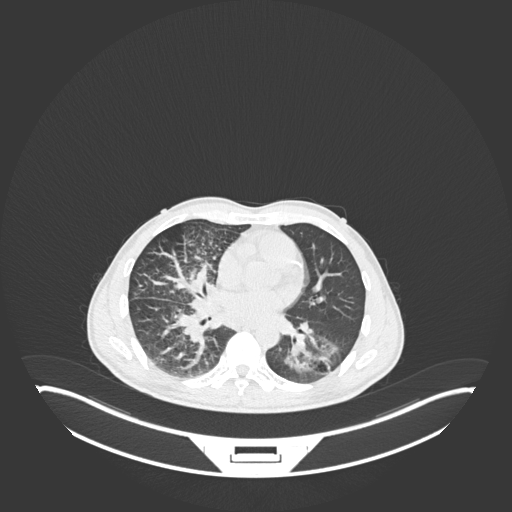
Chest CT, one axial slice; position 112 of 237 along the scan axis; 120 kVp; lung window (W 1500 / L -600 HU); 512 × 512 image matrix, field of view 500 × 500 mm. Patient: male, 49 years. Case-level facts recorded for this patient, not image findings: clinical TNM (as recorded): T2b N1 M0.
Annotated regions visible in this slice (rectangle marked by the reading radiologist):
- lung tumour (recorded histology: adenocarcinoma): bounding box [x1, y1, x2, y2] px = [283, 322, 343, 379]